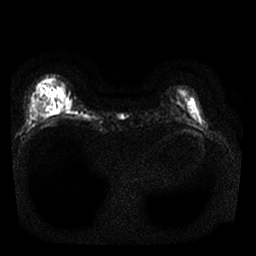
Breast MRI, one axial slice. Diffusion-weighted series; image 2 of 4 stored at this slice position (different b-values; order by instance number). 1.5 T. 256 × 256 image matrix, field of view 310 × 310 mm. Female patient.
Outlined on this slice (manually delineated by an expert):
- tumour on diffusion-weighted imaging: bounding box <65,100,71,108> (left, top, right, bottom; pixels)